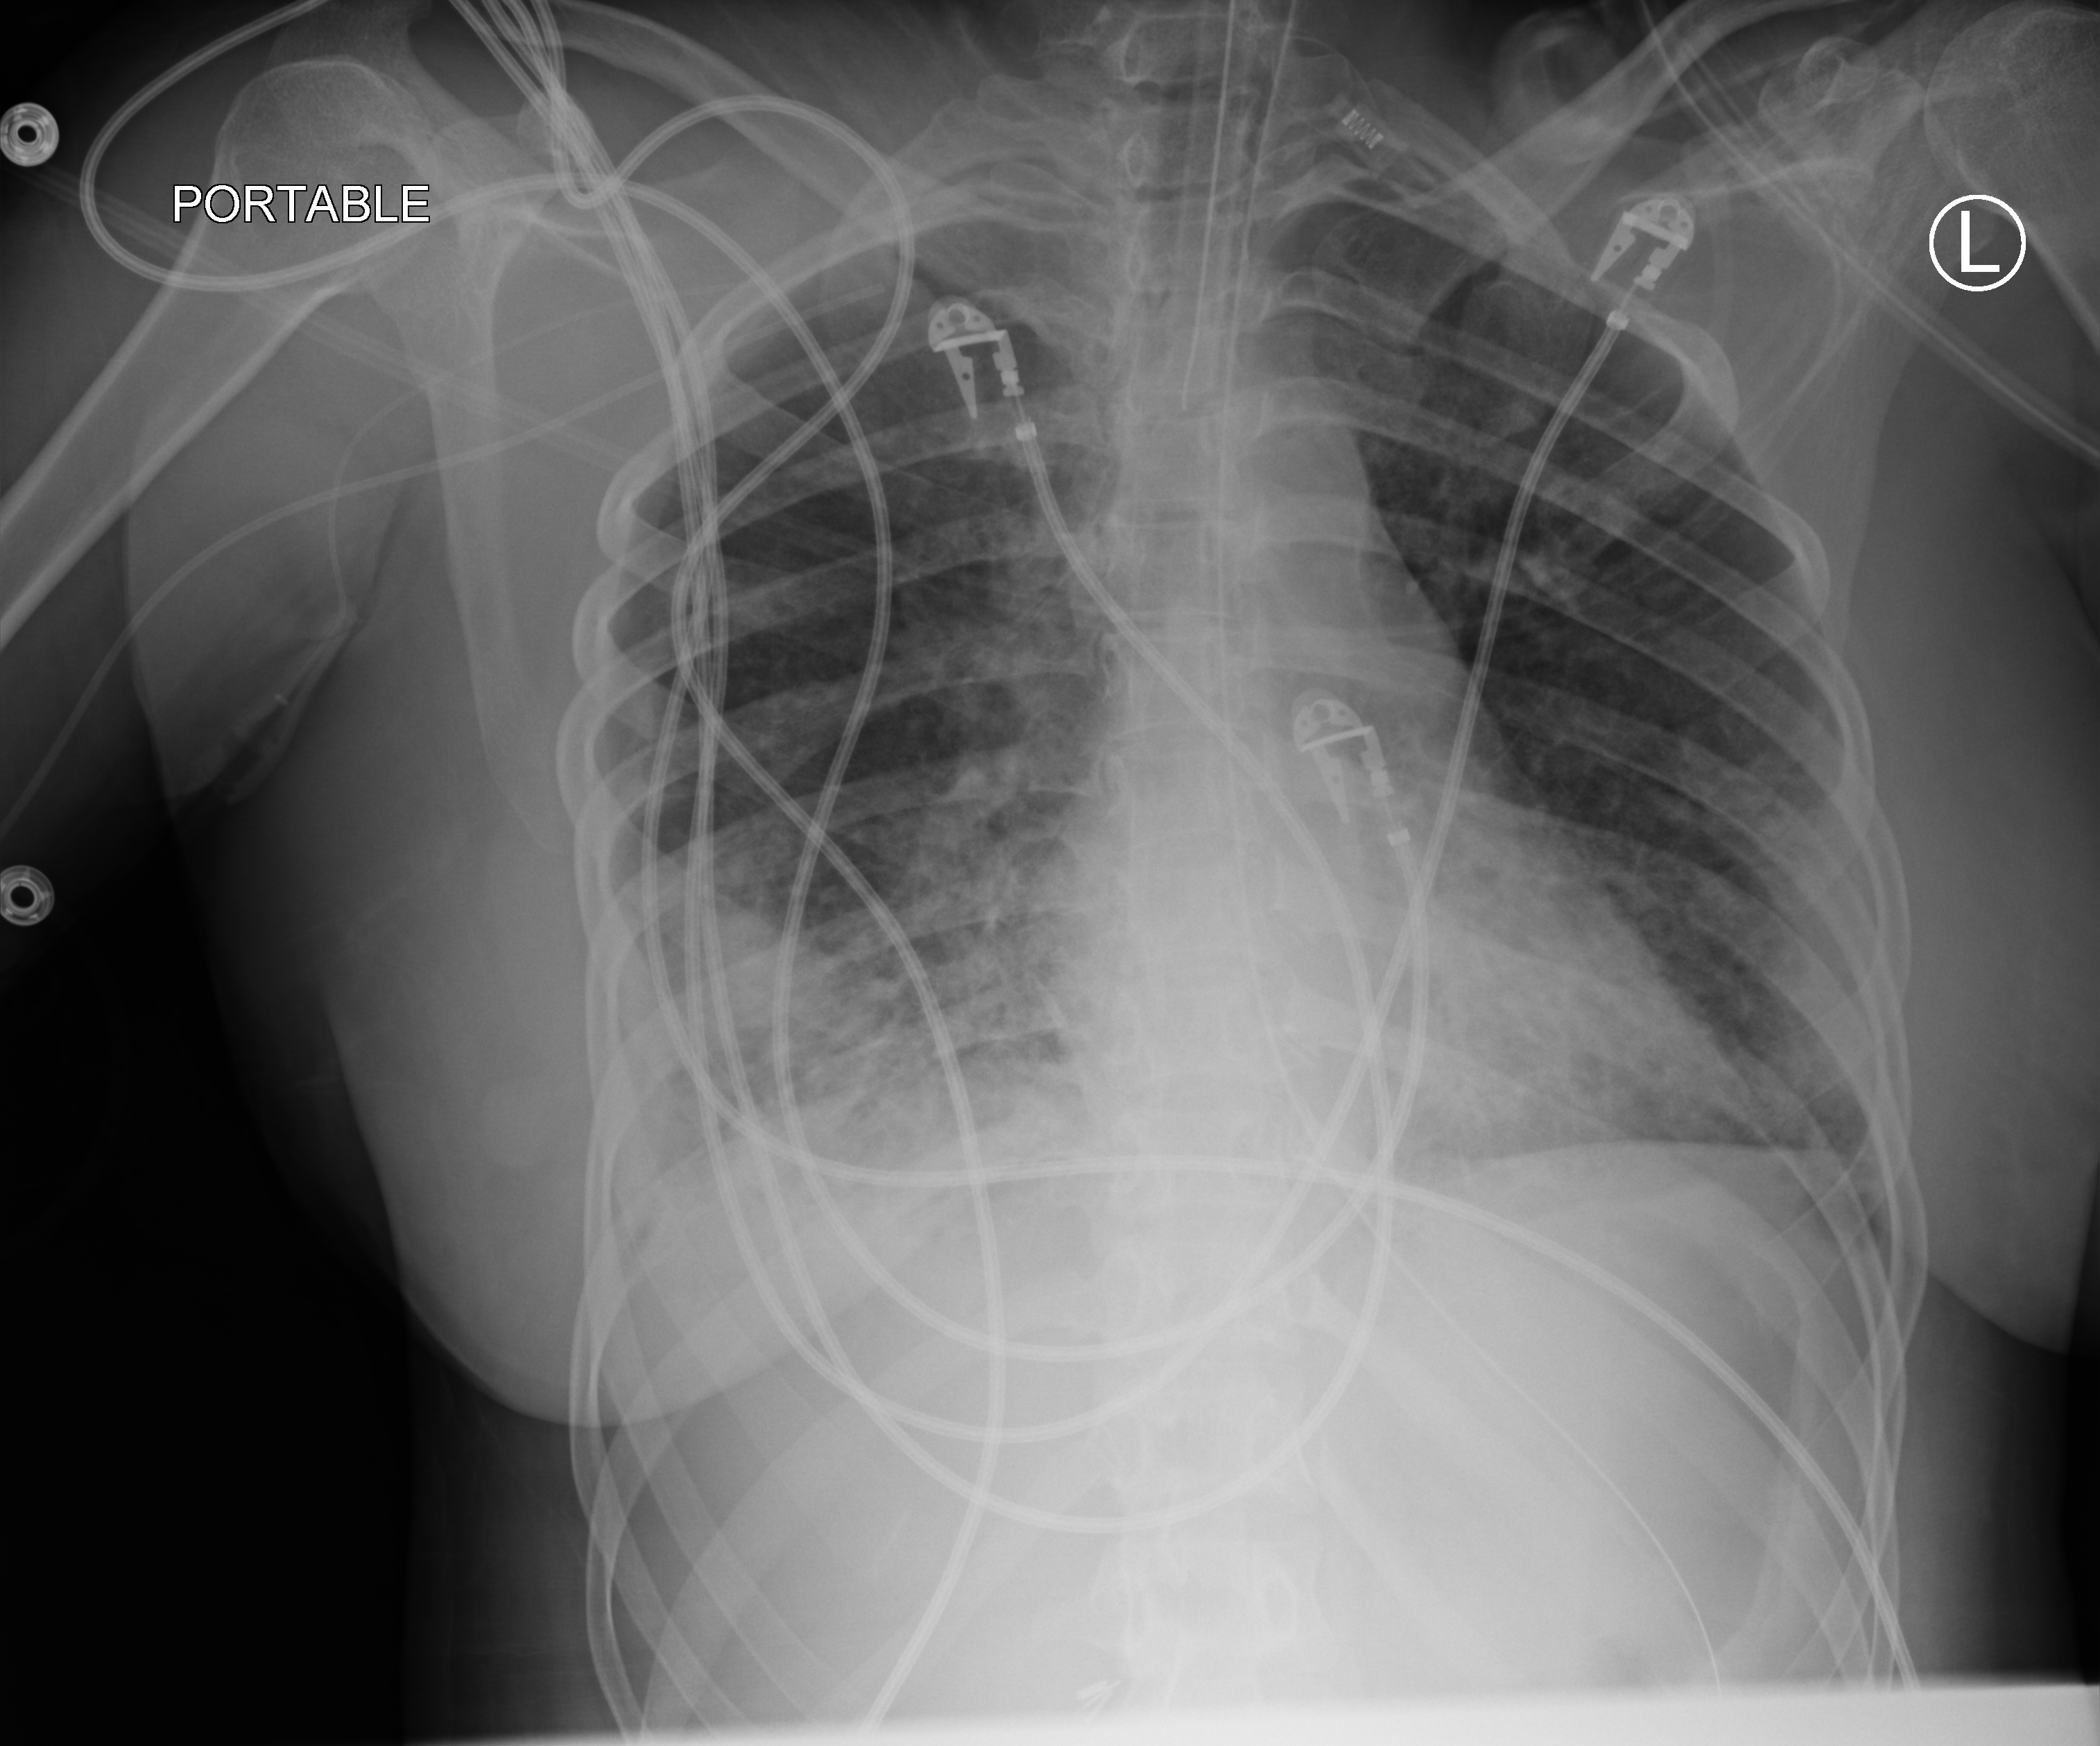
Chest X-ray (portable); anteroposterior (AP) projection. Patient hospitalised with COVID-19, aged 18–59 years.
Hospital-stay facts (about this admission, not read from this image; timing relative to this image not recorded): other chronic lung disease (admission record): no; mechanically ventilated during this hospital stay: yes.